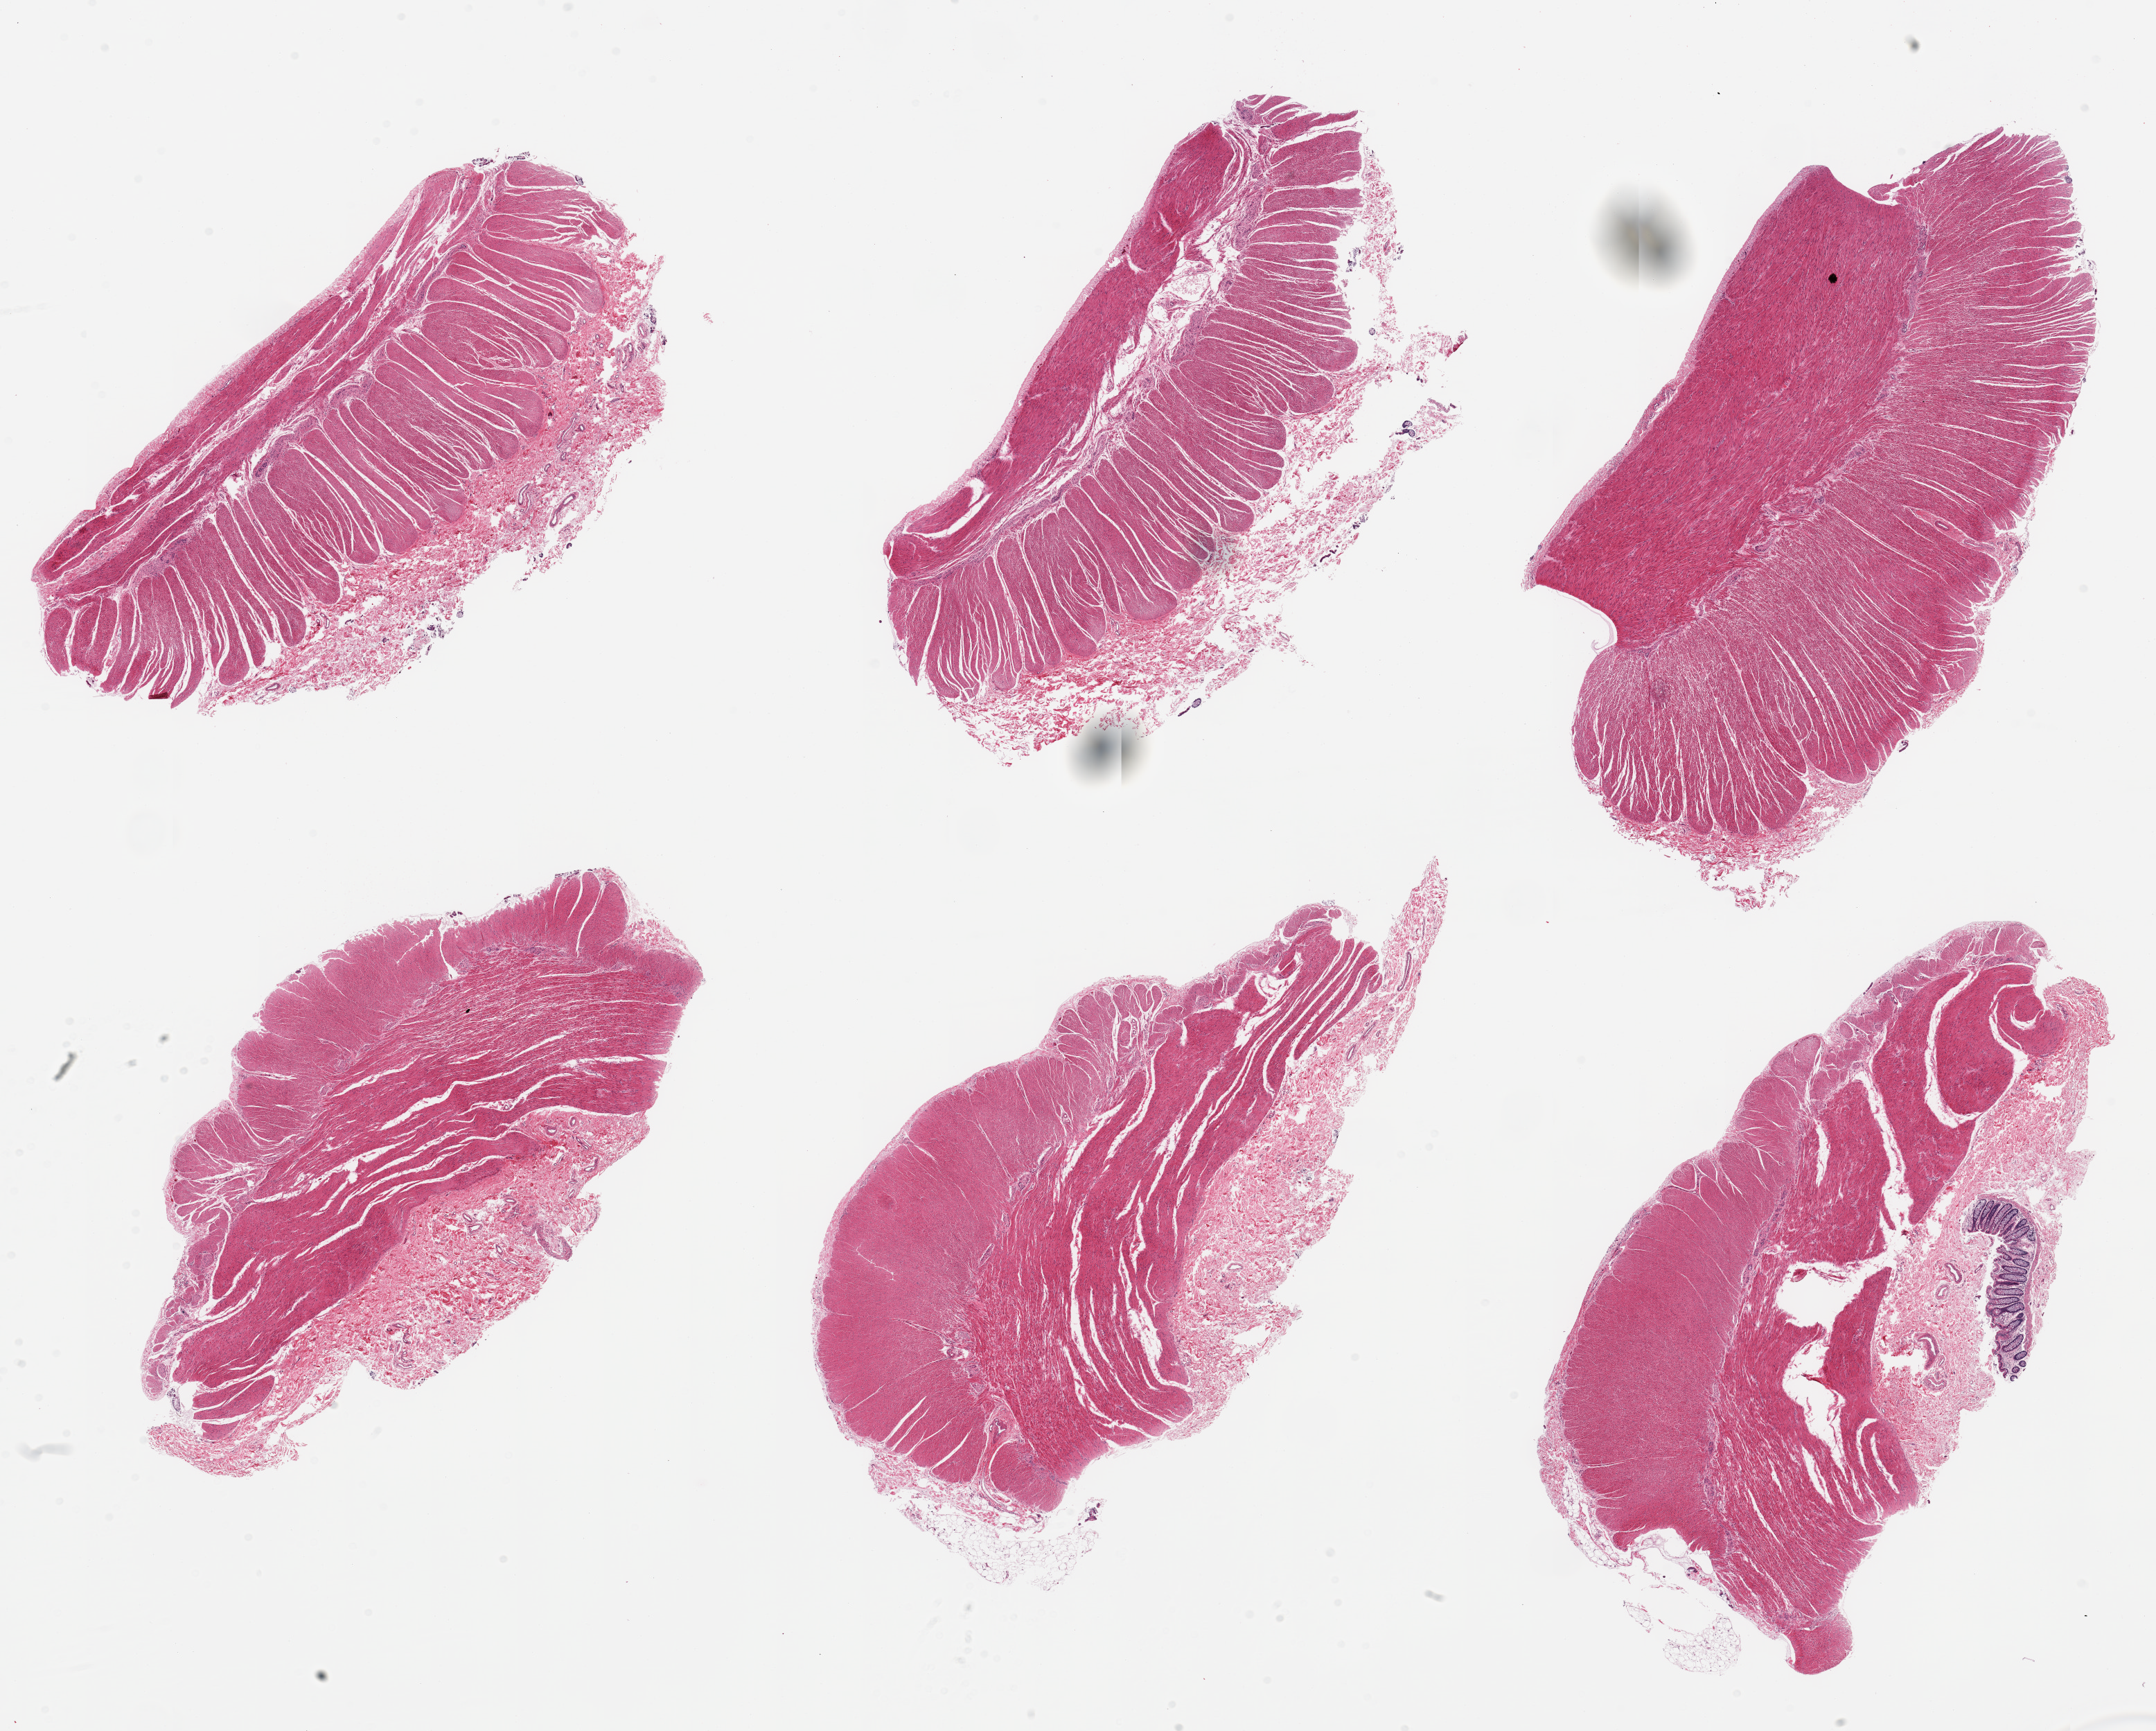
Haematoxylin and eosin whole-slide image, brightfield, whole scanned area (about 24.6 x 19.8 mm, from a 20x scan) shown as a low-resolution overview, PAXgene-fixed paraffin-embedded (PFPE) section, target tissue: sigmoid colon, tissue donor sample. Donor sex: male.
Pathologist's review note for this sample: 6 pieces; predominantly muscularis with residual submucosa and strip of mucosa in one piece.